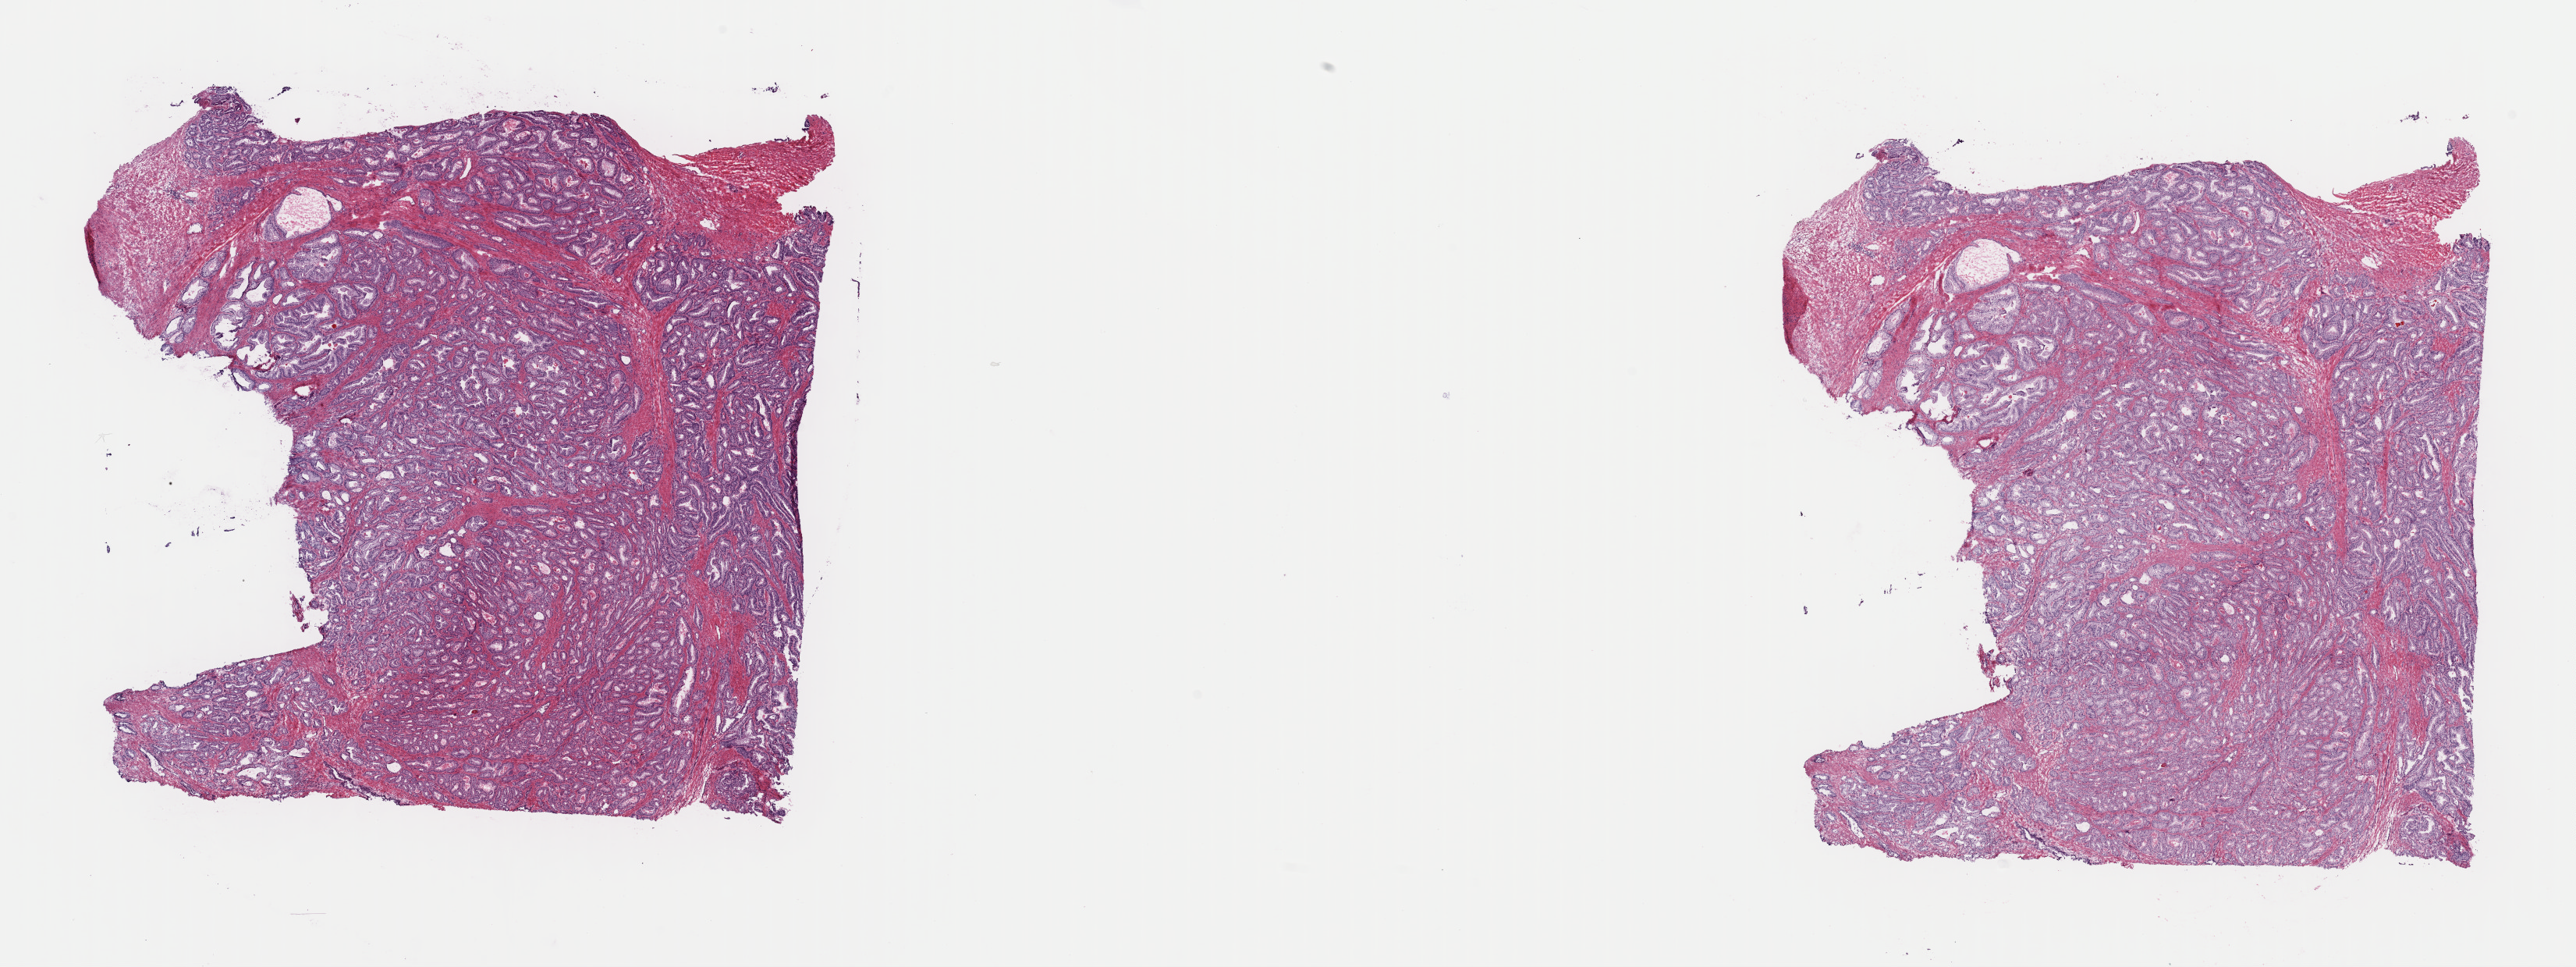
H&E whole-slide image — whole scanned area (about 26.1 x 9.8 mm) shown as a low-resolution overview, frozen section, sample: primary tumour, prostate. Male patient; age at initial diagnosis 71 years.
Histologic diagnosis: Acinar cell carcinoma (prostate gland).